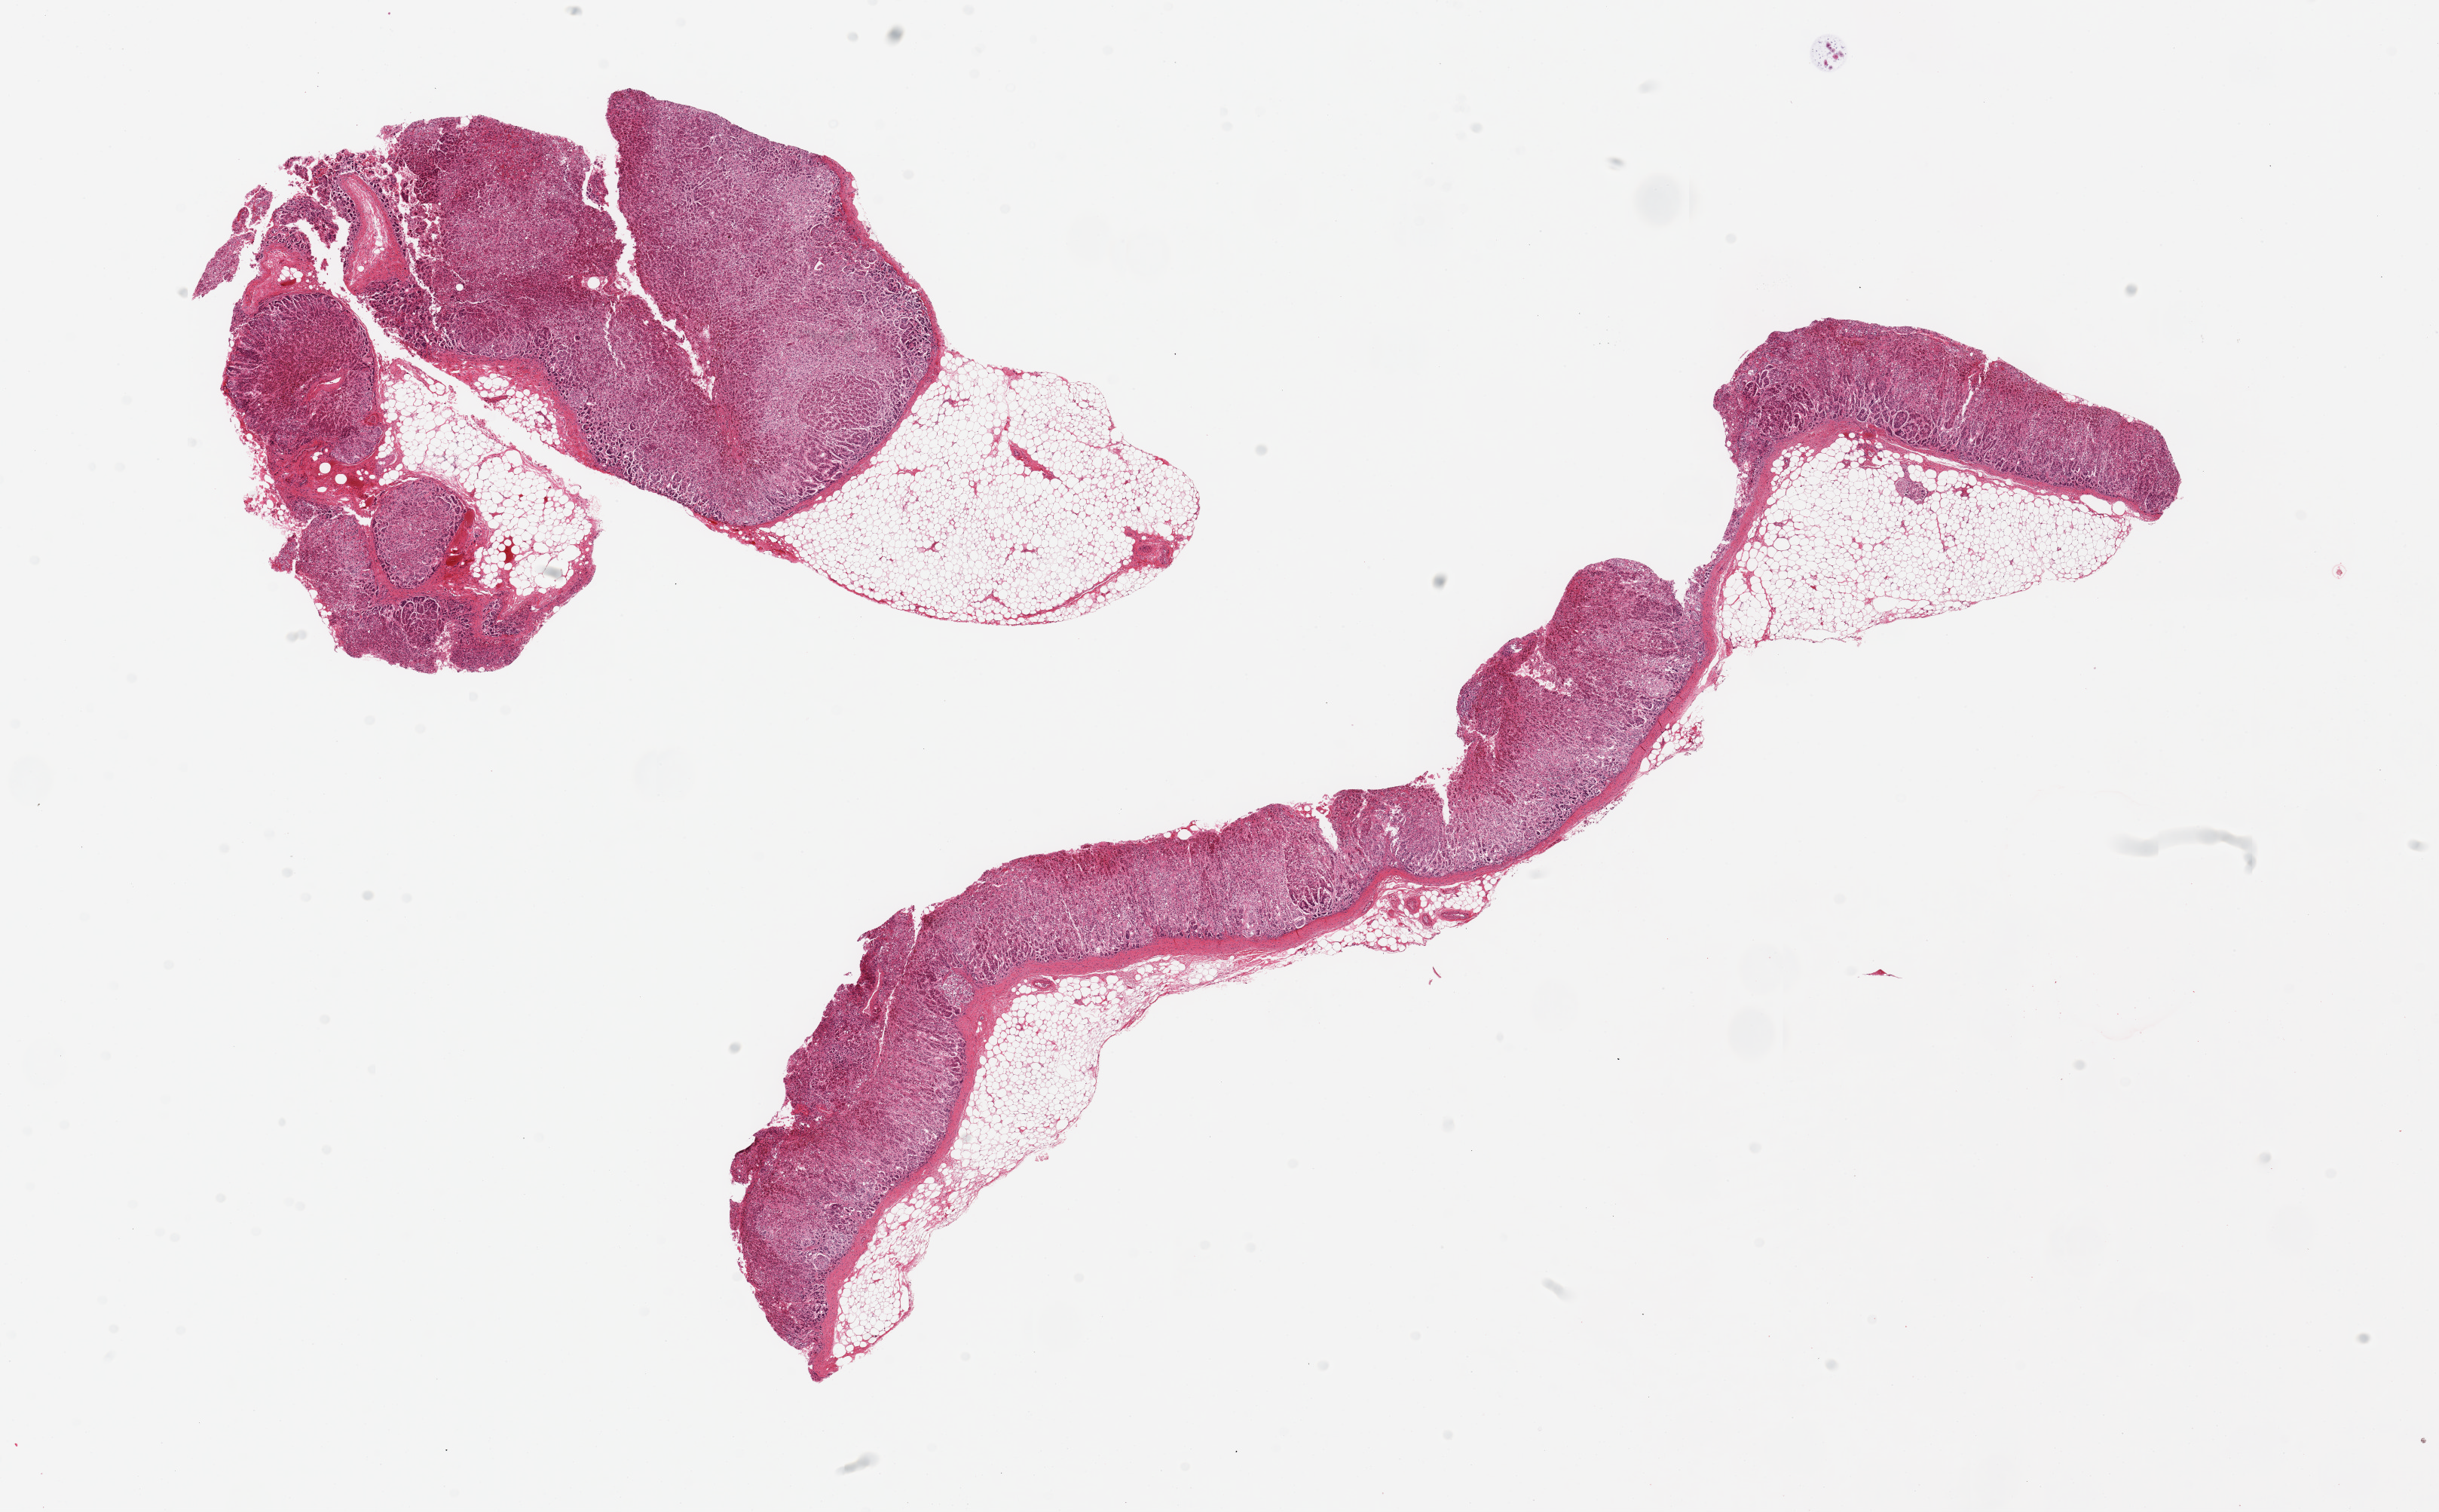
Hematoxylin and eosin (H&E) whole-slide image — low-resolution overview of the scanned area, about 25.6 x 15.9 mm. PAXgene-fixed, paraffin-embedded tissue. Target tissue: adrenal gland. Donor tissue sample. Male donor.
- review note (as recorded): 2 pieces ~13 x 3mm, ~30% adherent fat